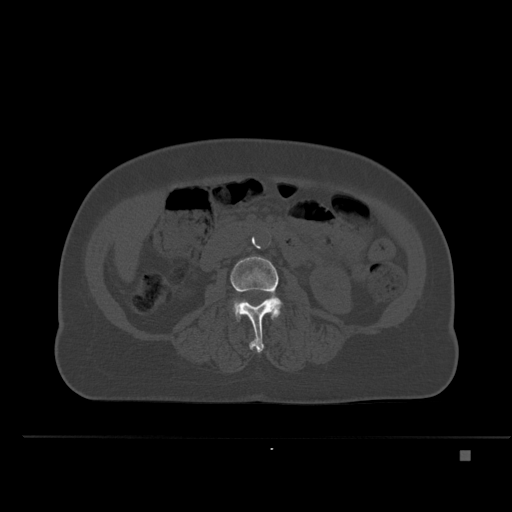
CT including the spine, one axial slice. Position 195 of 477 along the scan axis. Bone window (W 1800 / L 400 HU). 1.5 mm slice thickness. 512 × 512 image matrix. Female patient, age 74 years. Case-level facts recorded for this patient, not image findings: primary cancer: colon.
Structures marked on this image (semi-automatically segmented with operator editing):
- L3 vertebra: bounding box [x1, y1, x2, y2] px = [230, 256, 283, 353]
- L4 vertebra: [233, 300, 236, 313]